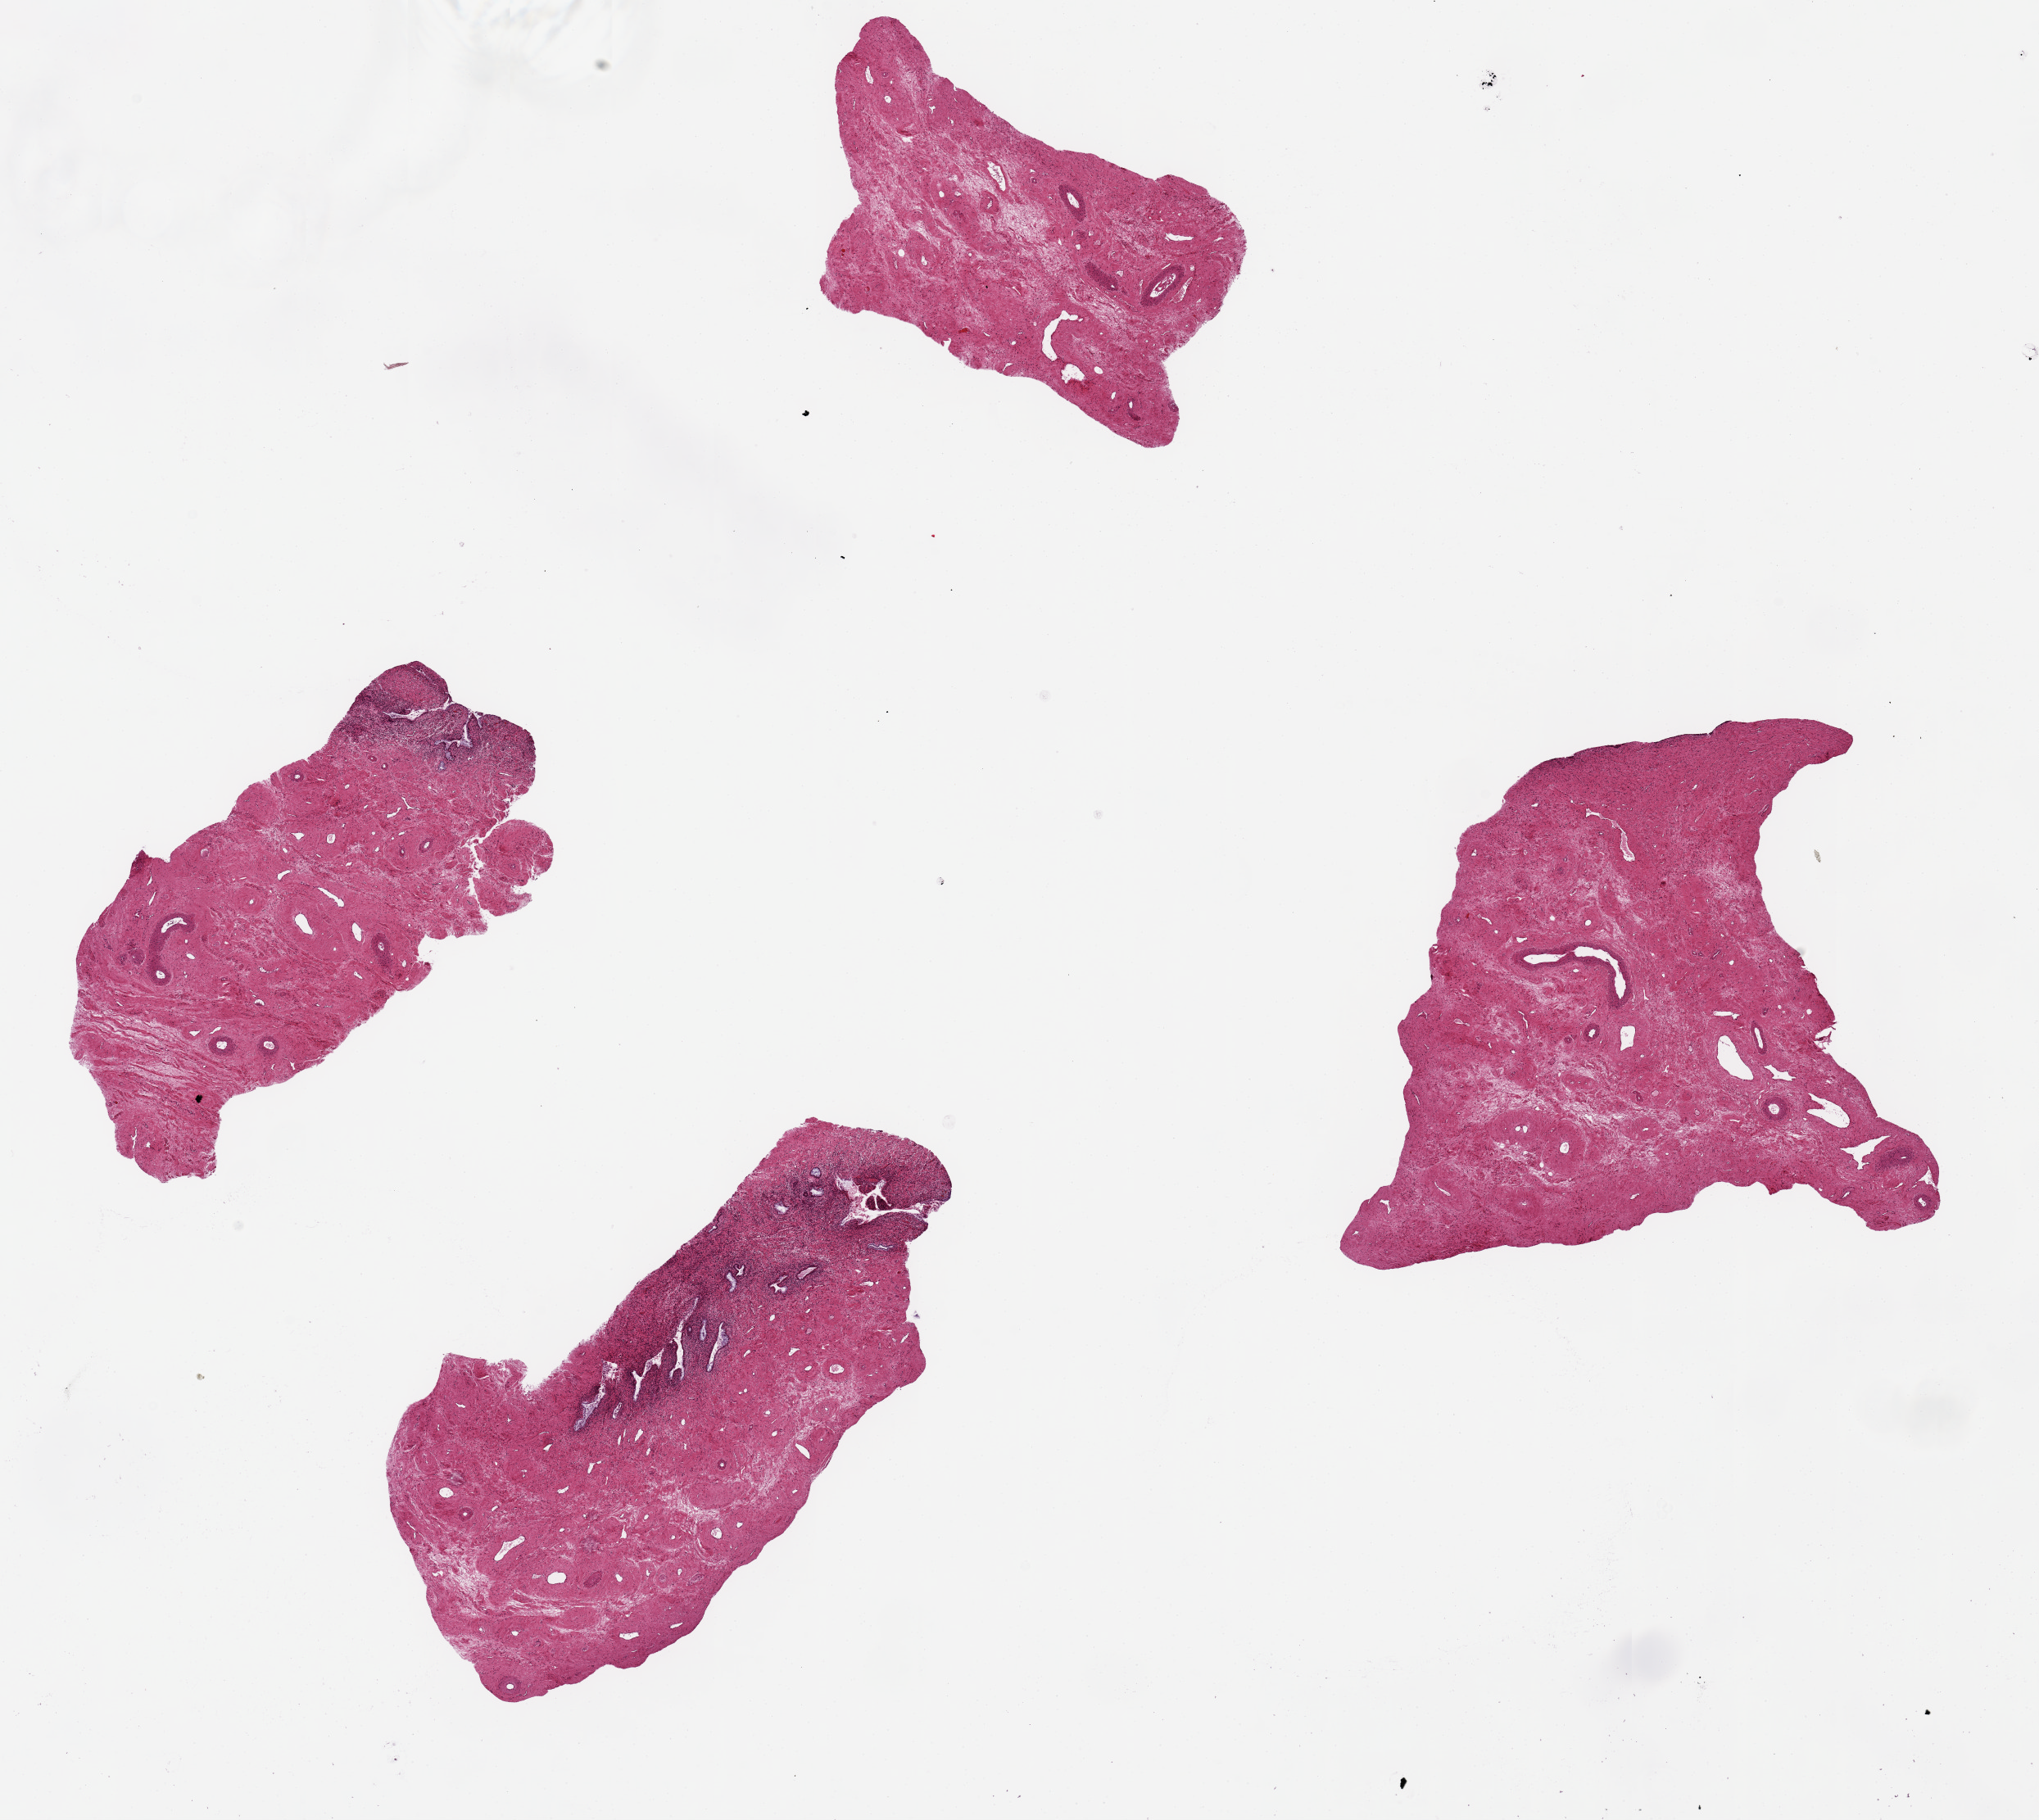
Digitized H&E-stained section, brightfield, a low-resolution overview of the entire scanned area, about 19.7 x 17.6 mm (acquisition: 20x scan), PAXgene-fixed, paraffin-embedded tissue, sampled site (target tissue): endocervix, donor tissue sample. Female donor.
* review note (as recorded): 4 pieces up to 6x3 mm; 2 pieces have endocervical glands, none has squamous; consider it endocervix